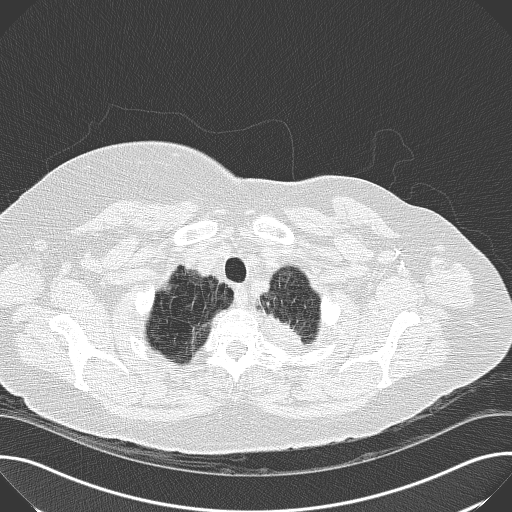
Low-dose screening chest CT, one axial slice. Slice 153 of 169 in the series (ordered by position). 120 kVp. Lung window (W 1500 / L -600 HU). 2 mm slice thickness. 512 × 512 image matrix, field of view 380 × 380 mm.
Outlined on this slice (expert manual segmentation):
- lesion 1 (tumor, upper lobe of left lung): bounding box <269,314,301,344> (left, top, right, bottom; pixels)